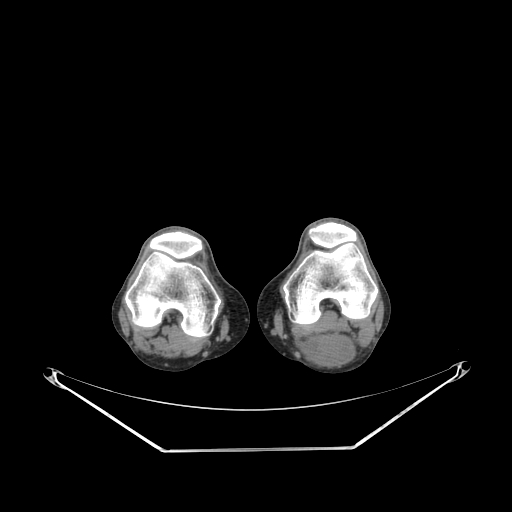
CT of an extremity soft-tissue mass (from a PET/CT study), one axial slice. Position 178 of 267 along the scan axis. 140 kVp. Soft-tissue window (W 400 / L 40 HU). 512 × 512 image matrix. Male patient. From the clinical record (not read from this slice): histological type: synovial sarcoma; site of the primary tumour: left poplietal fossa.
Annotated regions visible in this slice (expert contour drawn on MRI and transferred to this co-registered scan by the dataset authors):
- gross tumour volume (mass): bounding box <299,331,355,366> (left, top, right, bottom; pixels)